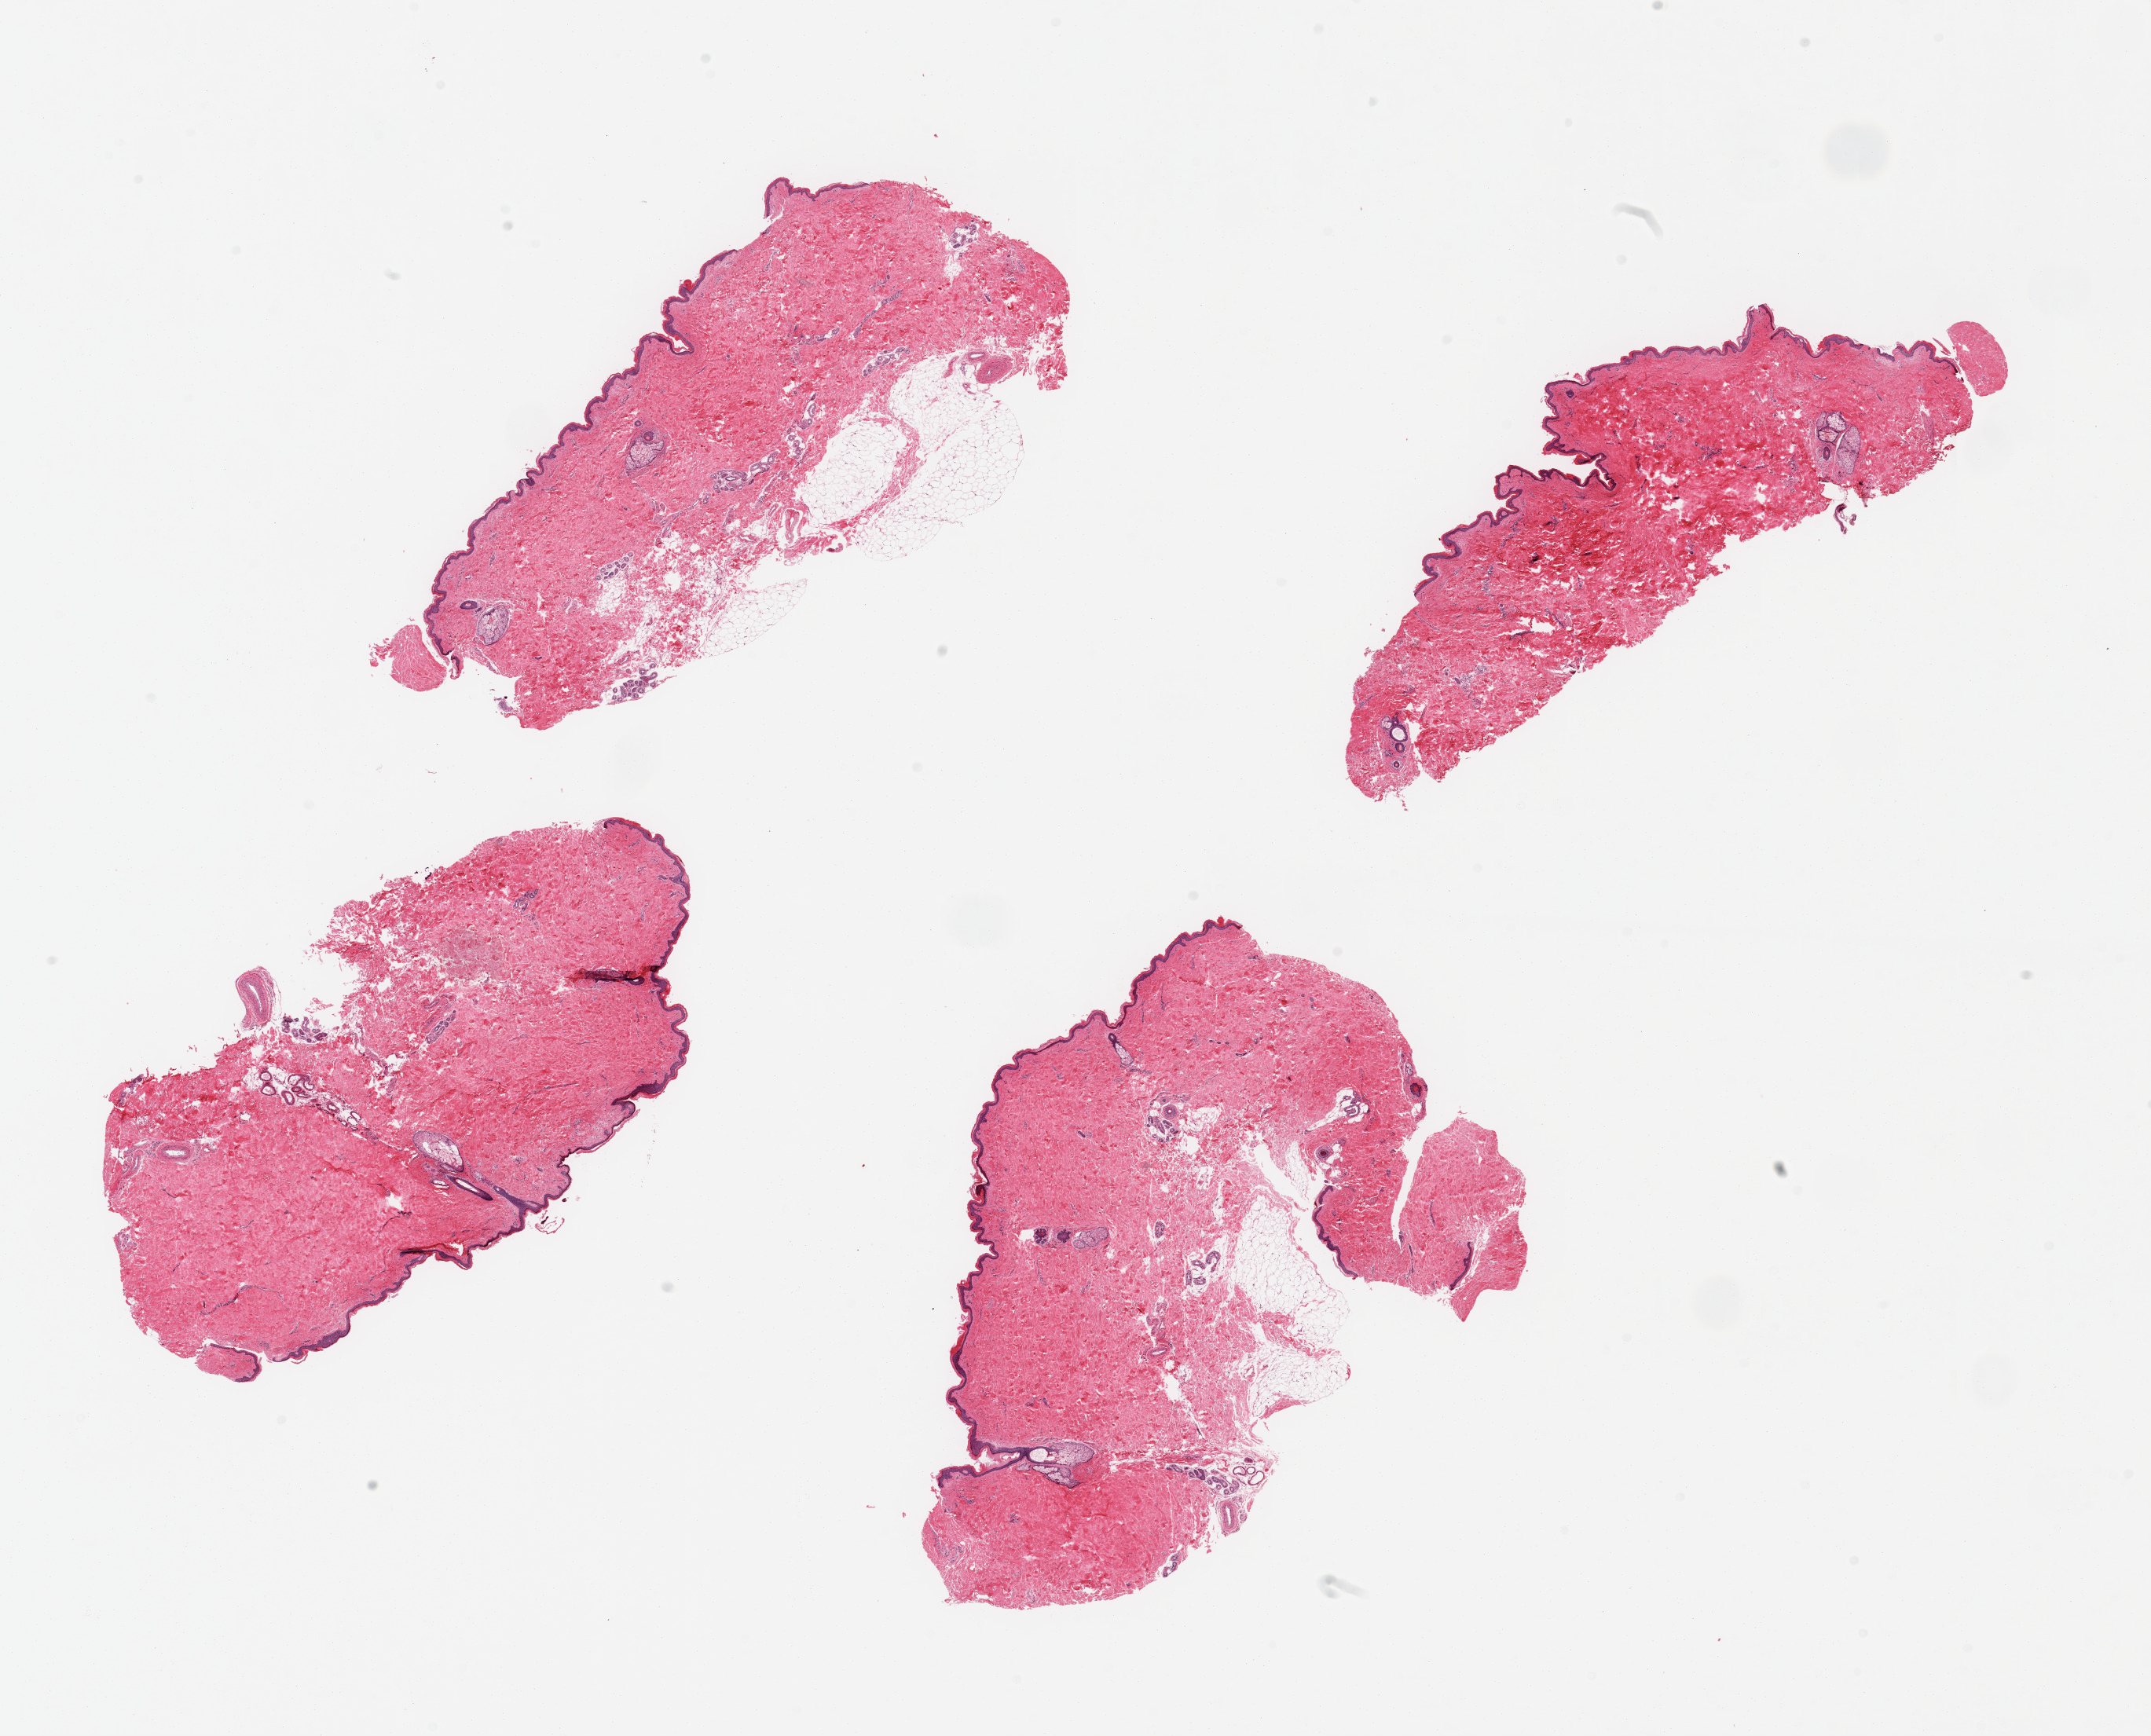
Whole-slide image, hematoxylin and eosin (H&E) stain — low-resolution overview of the scanned area, about 21.7 x 17.5 mm (slide scanned at 20x). PAXgene-fixed paraffin-embedded (PFPE) section. Section of skin of suprapubic region (target tissue). Donor tissue sample. Female donor.
Review note (as recorded): 4 pieces; well trimmed.